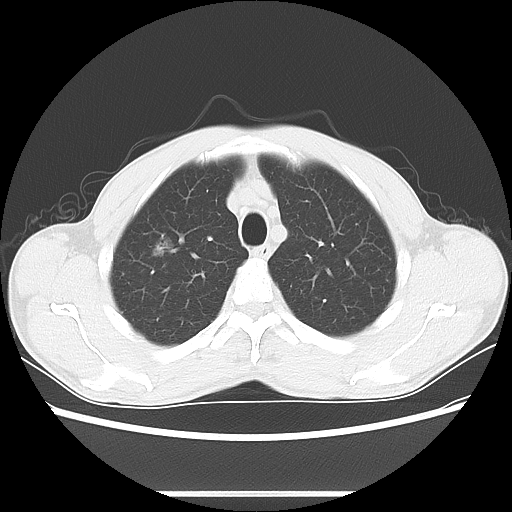
Chest CT, one axial slice. Slice 61 of 76 in the series (ordered by position). Reconstruction kernel LUNG. 100 kVp. Lung window (W 1500 / L -600 HU). 512 × 512 image matrix, field of view 357 × 357 mm. Male patient, age 54 years. From the clinical record (not read from this slice): clinical TNM (as recorded): T1a N0 M0.
Annotated regions visible in this slice (bounding box drawn by a radiologist):
- lung tumour (recorded histology: adenocarcinoma): bounding box <146,227,192,264> (left, top, right, bottom; pixels)